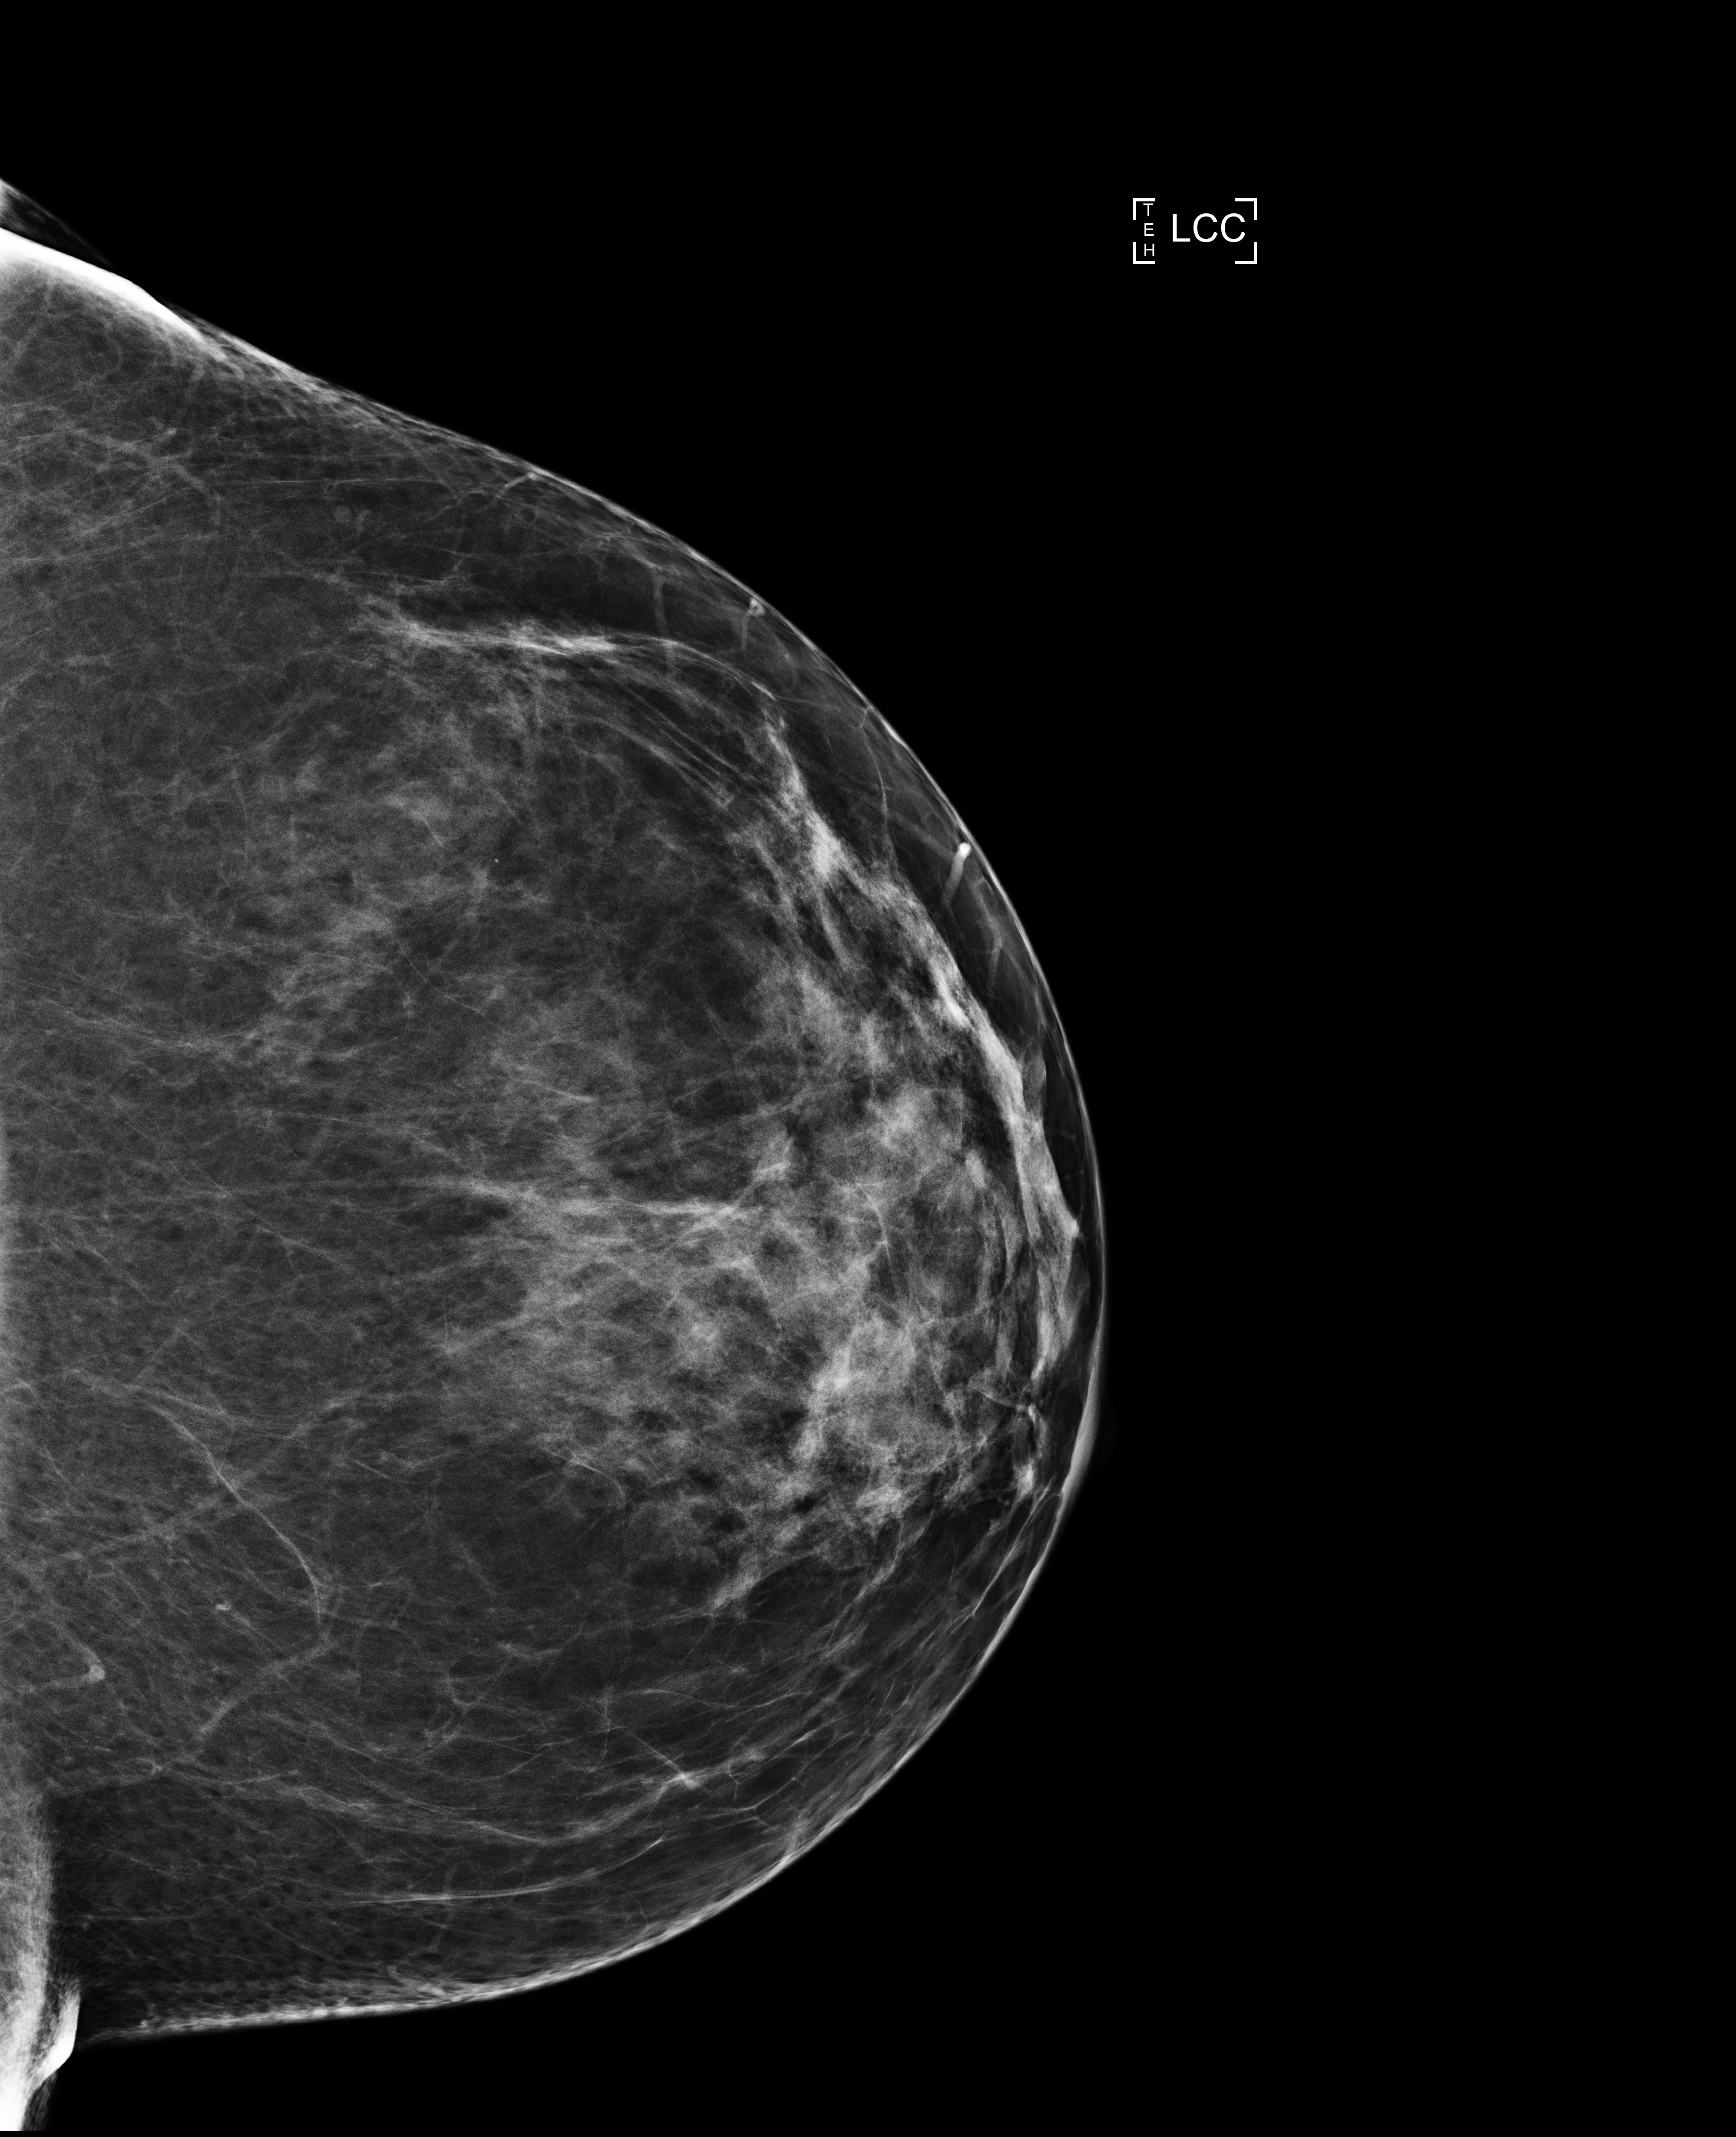
Screening examination. Female patient, age 65 years.
Image type: full-field digital mammogram. Breast: left. Projection: cranio-caudal projection.